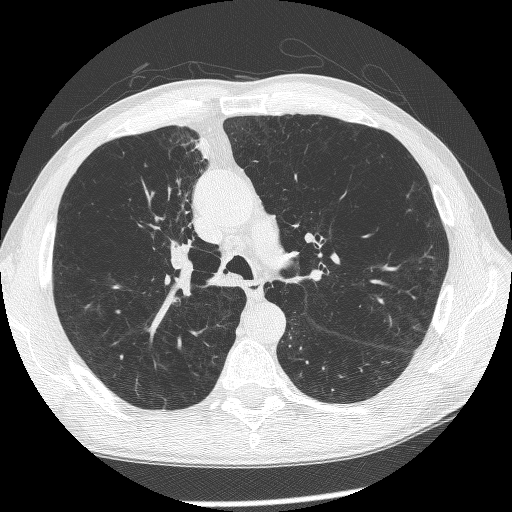
Axial slice from a low-dose chest CT screening exam, first (baseline) screen, lung window (W 1500 / L -600 HU), 1.25 mm slice thickness. Male participant, aged 60 years at enrolment.
Lesion marked by an expert reader, bounding box <143,215,228,308> (left, top, right, bottom; pixels). Screening reader's record for this exam (one nodule recorded; not confirmed to be the boxed lesion): non-calcified nodule or mass ≥4 mm, right upper lobe, 12 × 8 mm, spiculated (stellate) margins, mixed attenuation. Official screen result: positive, change unspecified: nodule(s) >= 4 mm or enlarging nodule(s), mass(es), or other non-specific abnormalities suspicious for lung cancer. Participant outcome: lung cancer diagnosed 208 days after this screen — squamous cell carcinoma, NOS, right upper lobe, right middle lobe, right main stem bronchus, poorly differentiated (G3), stage IV (AJCC 6th edition).